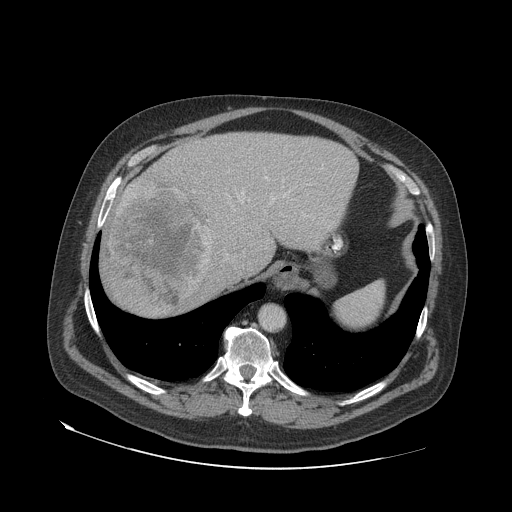
Contrast-enhanced abdominal CT (liver protocol), one axial slice; slice 57 of 79 in the series (ordered by position); reconstruction kernel STANDARD; soft-tissue window (W 400 / L 40 HU); 2.5 mm slice thickness; 512 × 512 image matrix, field of view 480 × 480 mm. Case-level facts recorded for this patient, not image findings: diagnosis: hepatocellular carcinoma (patient treated with transarterial chemoembolisation; whether this scan precedes or follows treatment is not stated here); TNM stage (as recorded): Stage-IVA; Child-Pugh class: A; tumour differentiation: well differentiated; tumour nodularity: multinodular.
Annotated regions visible in this slice (semi-automatic segmentation, software-assisted and operator-edited):
- abdominal aorta: bounding box (x1, y1, x2, y2) in pixels: (260, 305, 284, 329)
- liver parenchyma outside the tumour (the mass and vessels are separate outlines, so this box may not span the whole liver): (100, 132, 358, 316)
- mass: (105, 178, 213, 312)
- liver vessels: (239, 176, 309, 202)